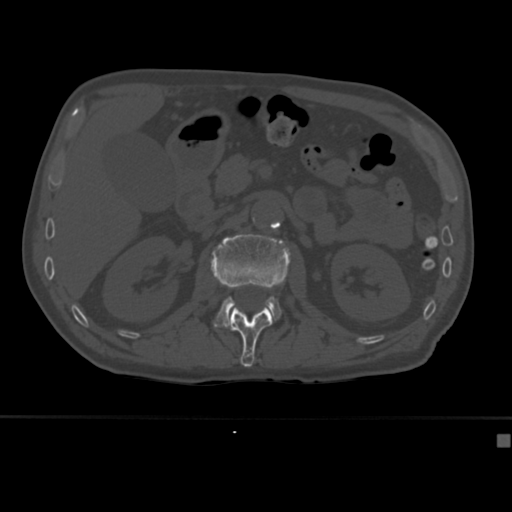
CT including the spine, one axial slice. Slice 160 of 430 in the series (ordered by position). 120 kVp. Bone window (W 1800 / L 400 HU). 512 × 512 image matrix, field of view 337 × 337 mm. Patient: male, 64 years. Case-level facts recorded for this patient, not image findings: primary cancer: uterus; vertebrae with lytic lesions (as recorded): T1, T4, T5, T7, L5.
Annotated regions visible in this slice (semi-automatic segmentation, software-assisted and operator-edited):
- L1 vertebra: bounding box <228,307,272,367> (left, top, right, bottom; pixels)
- L2 vertebra: <210,234,291,327>